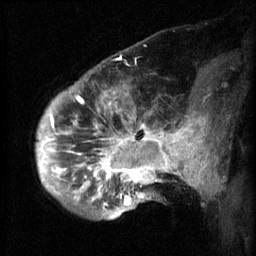
Breast MRI (dynamic contrast-enhanced), one sagittal slice; position 16 of 60 along the scan axis; 3 images stored at this slice position (order not interpretable as contrast timing); 1.5 T; TE 4.2 ms, TR 8.2 ms; 2.3 mm slice thickness; 256 × 256 image matrix, field of view 200 × 200 mm. Female patient, age 50 years.
Structures marked on this image (semi-automatic segmentation, software-assisted and operator-edited):
- analysis volume of interest (the breast-tissue region the enhancement analysis was run in; not a lesion): bounding box <50,66,169,217> (left, top, right, bottom; pixels)
- tumour enhancement mask (voxels above the 70 % enhancement threshold inside the analysis volume of interest): <50,92,169,207>